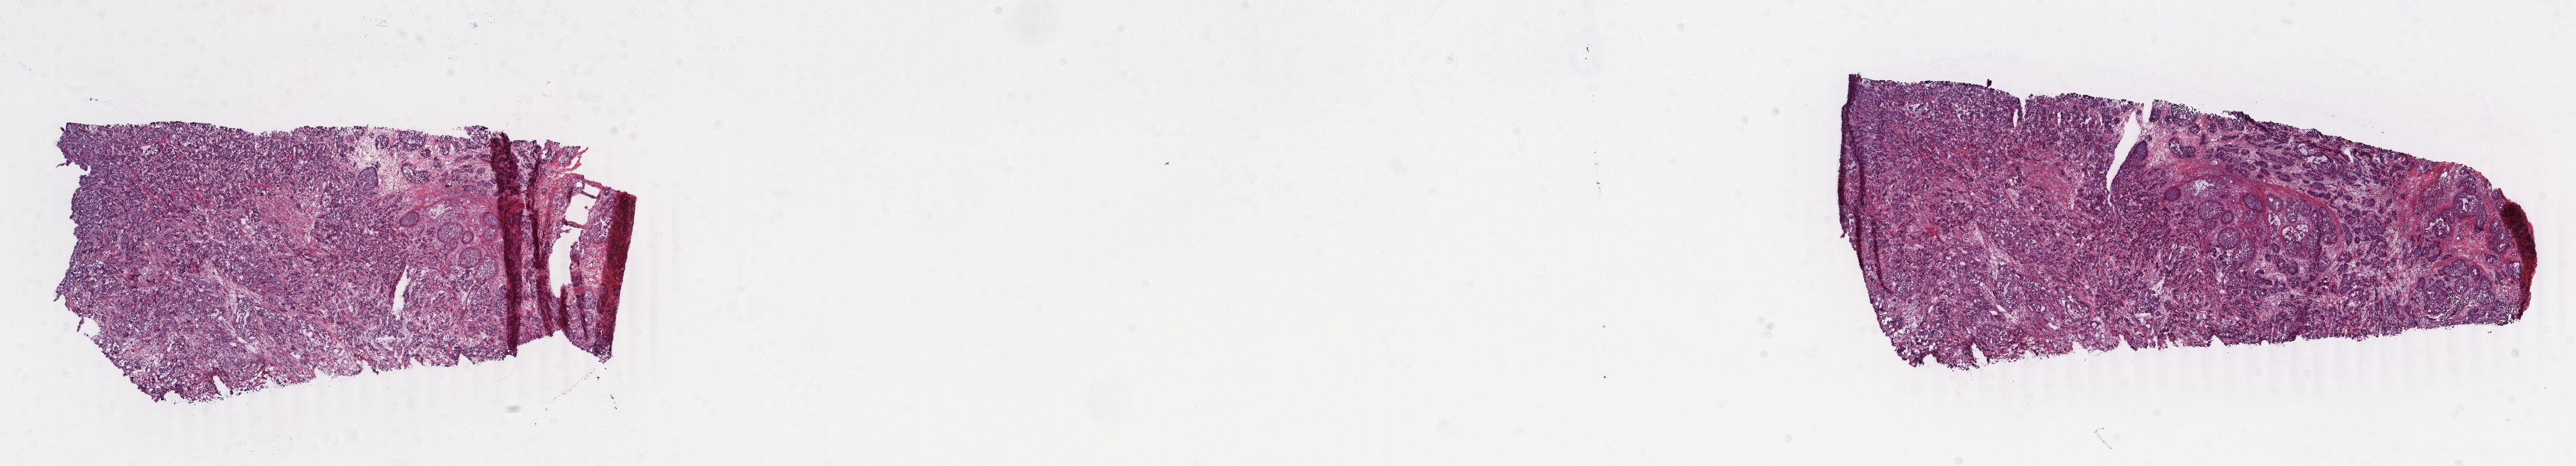
Whole-slide histology image, H&E — a low-resolution overview of the entire scanned area, about 27.4 x 4.9 mm; frozen section; primary tumour sample from the breast. Female patient; age at initial diagnosis 36 years. Pathologist review of this section (percent, as recorded): tumour cells 67%, tumour nuclei 70%, normal cells 15%, stromal cells 16%, necrosis 2%. Infiltration values recorded for this section: lymphocyte infiltration 13%, monocyte infiltration 1%, neutrophil infiltration 0%.
- AJCC pathologic stage: IIIA (7th edition)
- histologic diagnosis: Infiltrating duct carcinoma, NOS
- lymph nodes positive (case pathology): 4 of 7 examined